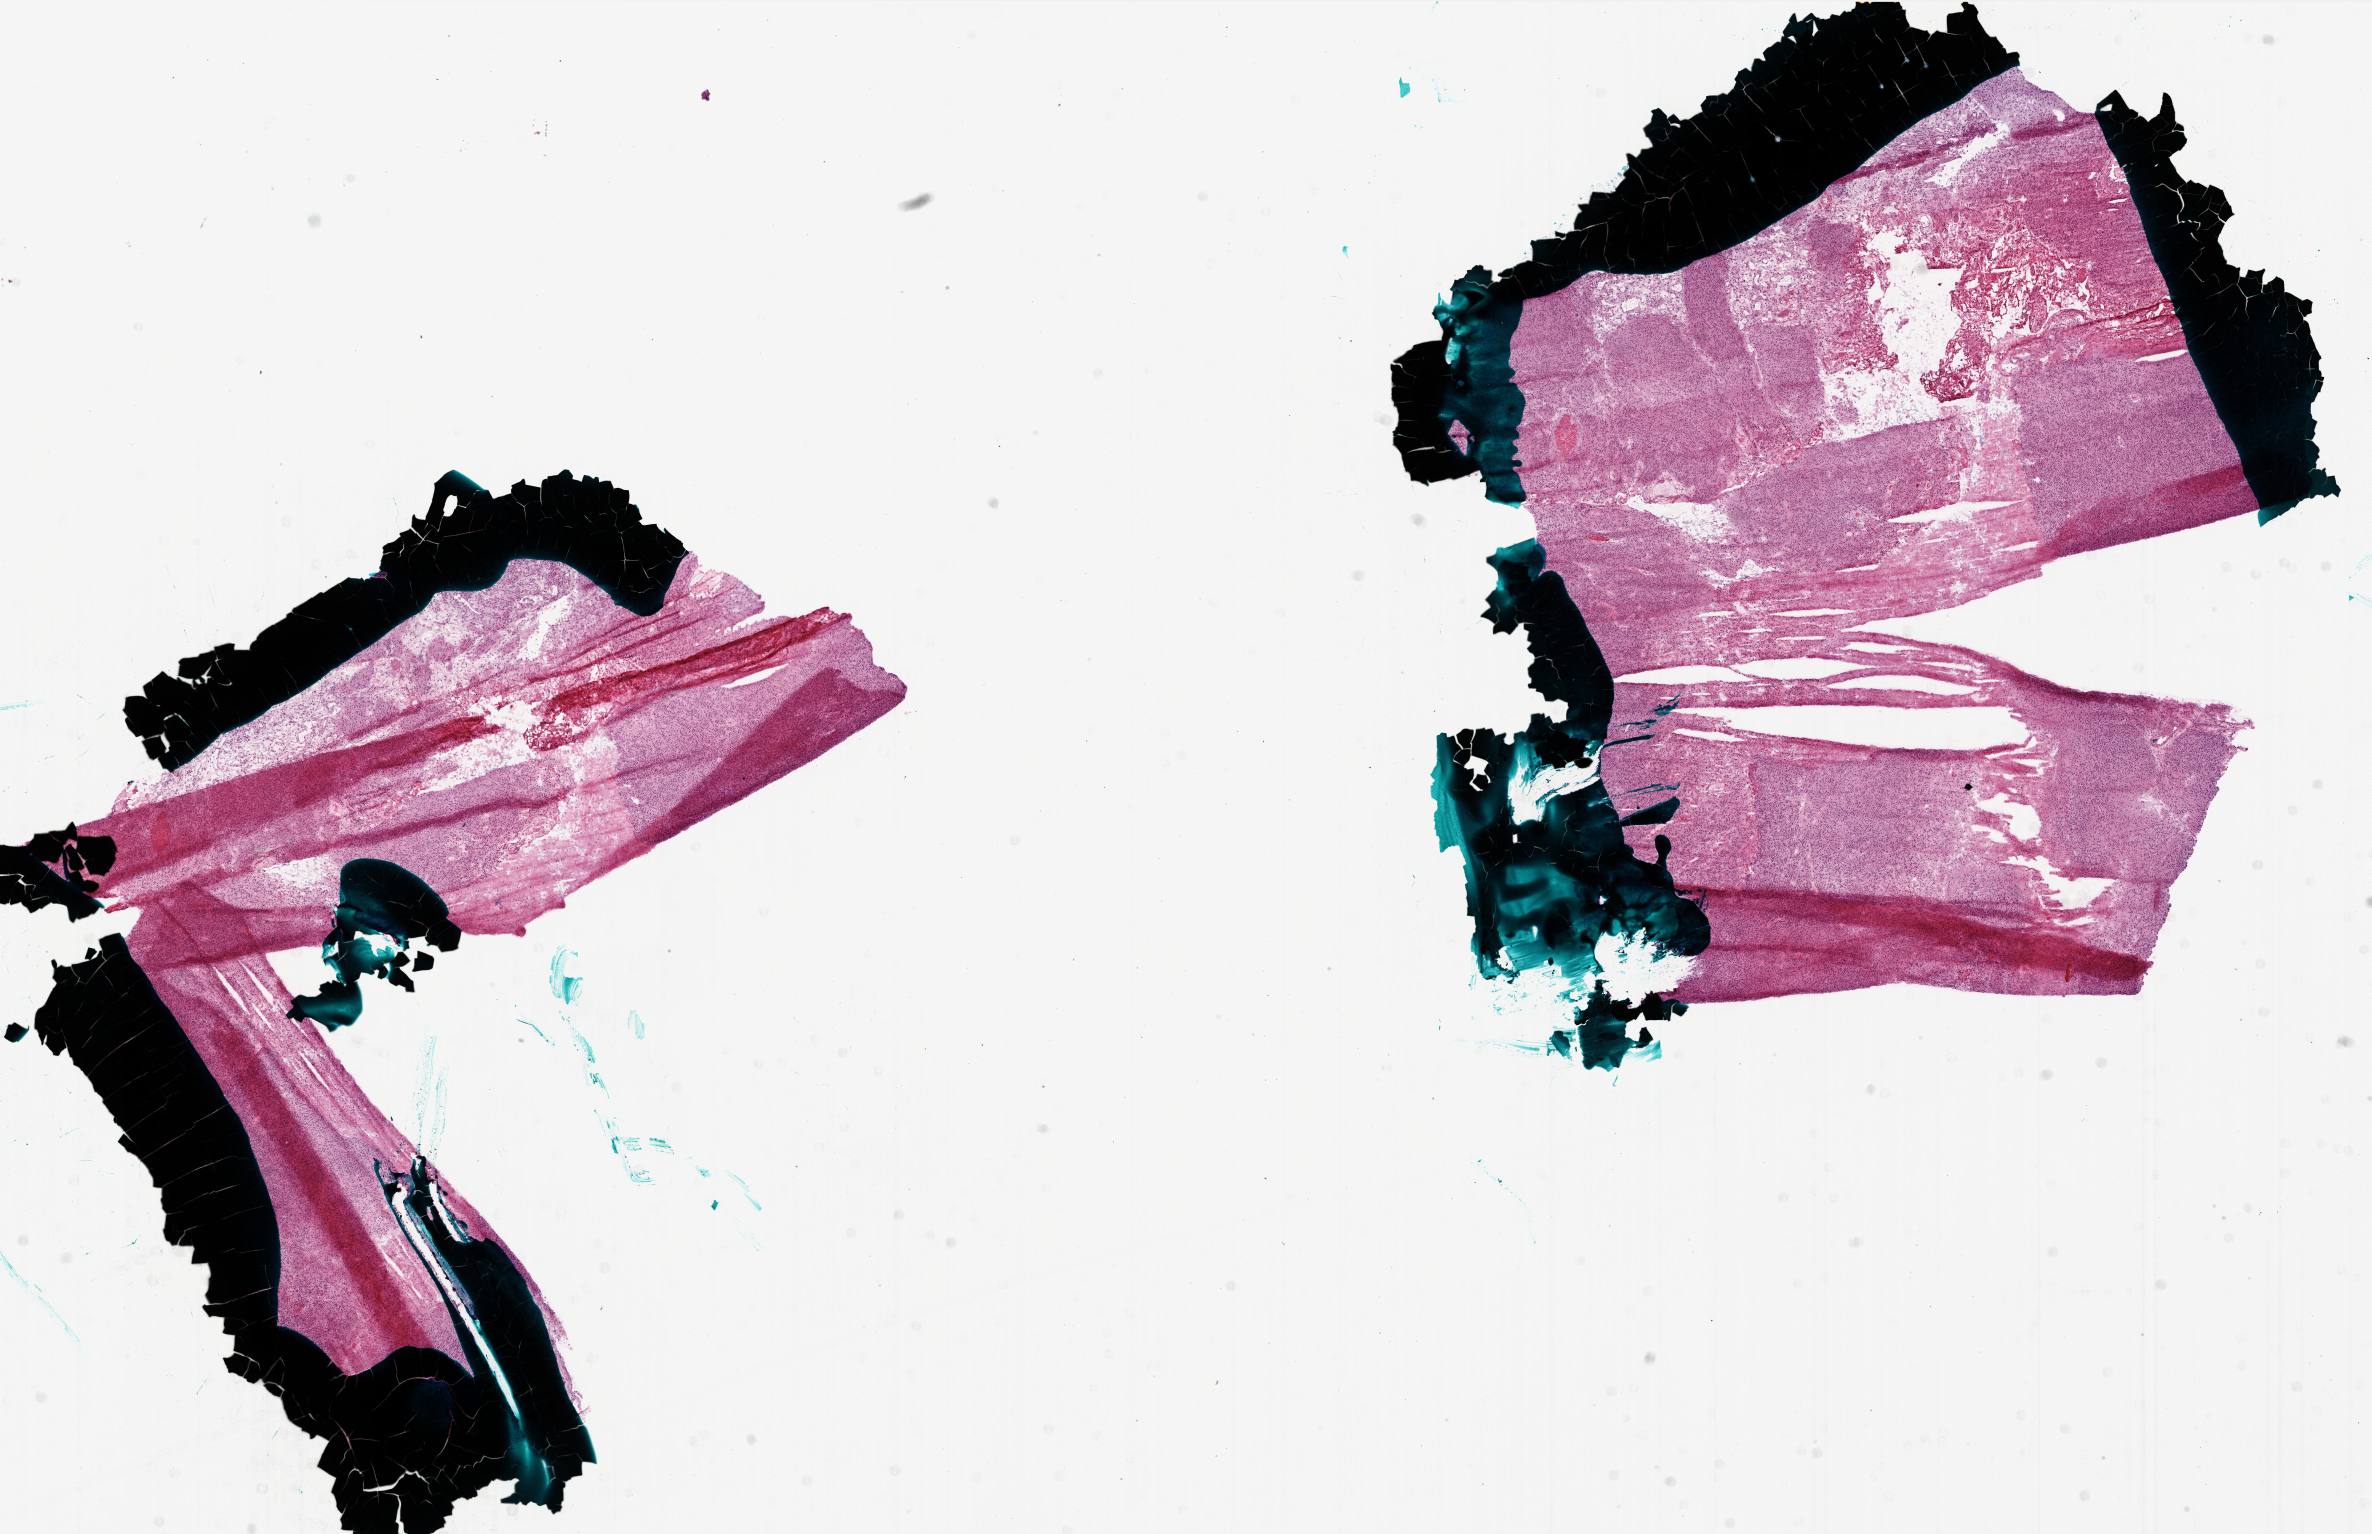
Digitized Hematoxylin and eosin (H&E) stained tissue section (whole slide) — shown as a low-resolution overview of the whole scanned area (about 19.0 x 12.3 mm, acquisition: 20x scan), frozen section from the bottom of the tissue portion, brain, primary tumour sample. Male patient; age at initial diagnosis 76 years. Pathologist review of this section (percent, as recorded): tumour cells 80%, tumour nuclei 100%, normal cells 0%, stromal cells 0%, necrosis 20%. Inflammatory infiltration, as recorded: lymphocyte infiltration 0%, monocyte infiltration 0%, neutrophil infiltration 0%.
Pathologic diagnosis: Glioblastoma.